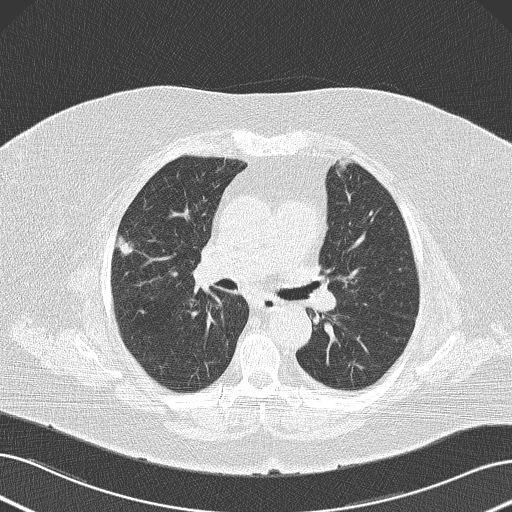
Low-dose screening chest CT, one axial slice; position 80 of 145 along the scan axis; 120 kVp; lung window (W 1500 / L -600 HU); 512 × 512 image matrix.
Structures marked on this image (expert manual segmentation):
- lesion 1 (tumor, upper lobe of right lung): bounding box [x1, y1, x2, y2] px = [117, 235, 136, 257]